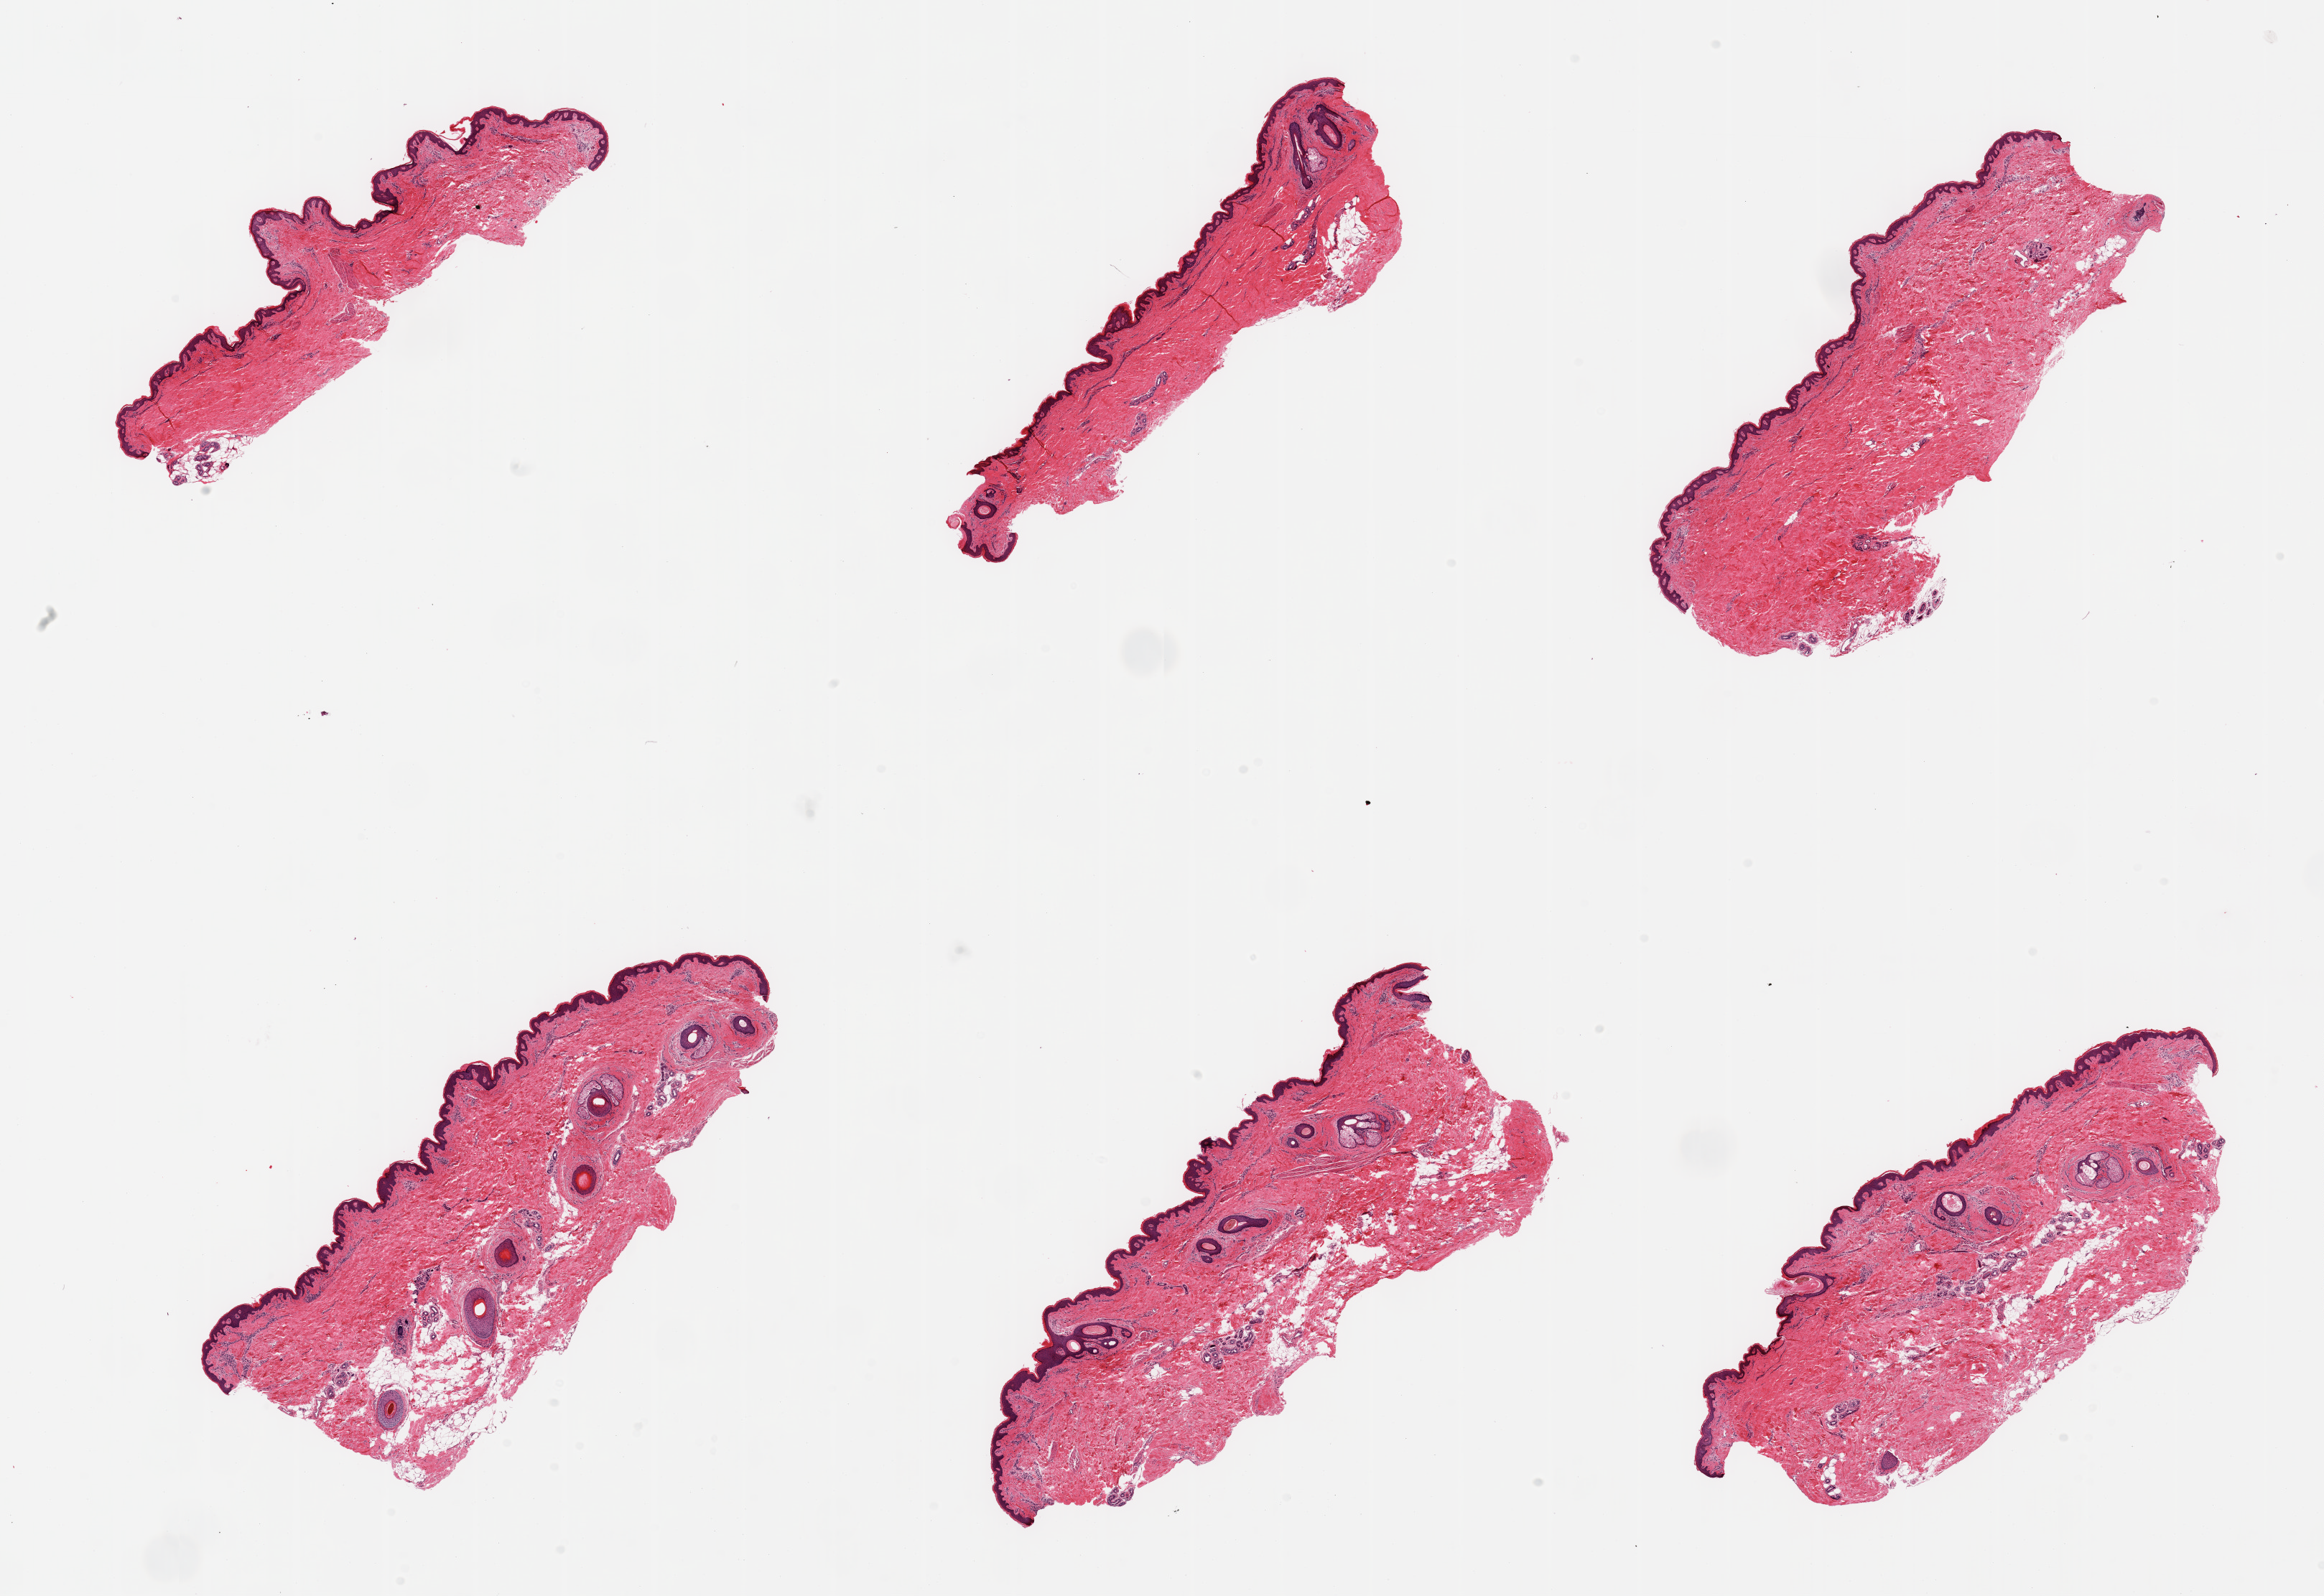
Whole-slide image, haematoxylin and eosin stain — low-resolution overview of the scanned area, about 25.6 x 17.6 mm, PAXgene-fixed, paraffin-embedded tissue, target tissue: skin of suprapubic region, donor tissue sample. Donor sex: male.
Pathologist's review note for this sample: 6 pieces; 3 have up to 7 hair follicles and 10% dermal fat.